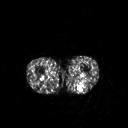
FDG PET of an extremity soft-tissue mass (from a PET/CT study), one axial slice. Position 201 of 267 along the scan axis. 3.27 mm slice thickness. 128 × 128 image matrix. Patient: male, 54 years. Case-level facts recorded for this patient, not image findings: histological type: synovial sarcoma; site of the primary tumour: left poplietal fossa.
Structures marked on this image (expert contour drawn on MRI and transferred to this co-registered scan by the dataset authors):
- gross tumour volume (mass): bounding box <77,81,84,91> (left, top, right, bottom; pixels)